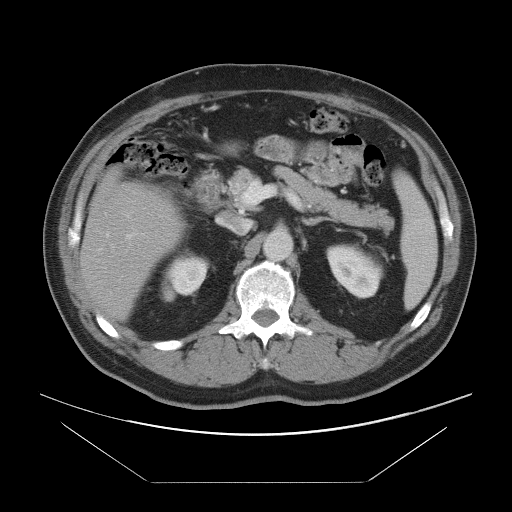
Contrast-enhanced abdominal CT, one axial slice; slice 47 of 97 in the series (ordered by position); intravenous contrast given; soft-tissue window (W 400 / L 40 HU); 5 mm slice thickness; 512 × 512 image matrix, field of view 442 × 442 mm. Male patient, age 62 years. From the clinical record (not read from this slice): diagnosis: colorectal cancer liver metastases, imaged before liver resection; multiple liver metastases: no.
Structures marked on this image (outlined manually by an expert reader):
- hepatic veins: bounding box (x1, y1, x2, y2) in pixels: (106, 233, 113, 247)
- liver: (82, 175, 181, 318)
- planned liver remnant (the part of the liver to remain after resection): (81, 176, 180, 318)
- portal vein (with intrahepatic branches): (127, 235, 132, 238)